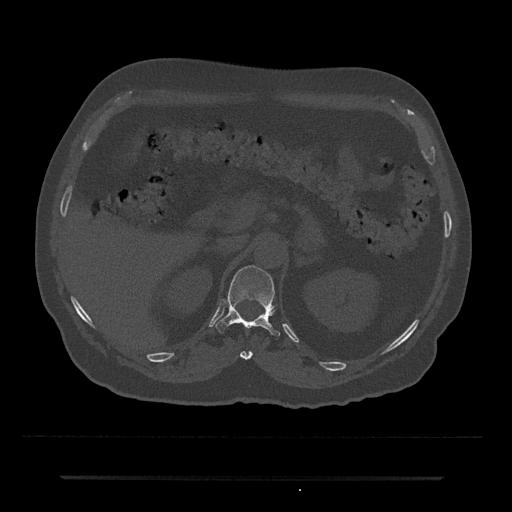
CT including the spine, one axial slice. Position 133 of 797 along the scan axis. Reconstruction kernel Br40s/3. Bone window (W 1800 / L 400 HU). 0.5 mm slice thickness. 512 × 512 image matrix, field of view 437 × 437 mm. Patient: male, 69 years. Case-level facts recorded for this patient, not image findings: primary cancer: prostate.
Structures marked on this image (semi-automatically segmented with operator editing):
- T11 vertebra: box from (x=240, y=351) to (x=253, y=360) px
- T12 vertebra: (x=215, y=265)–(x=281, y=336)